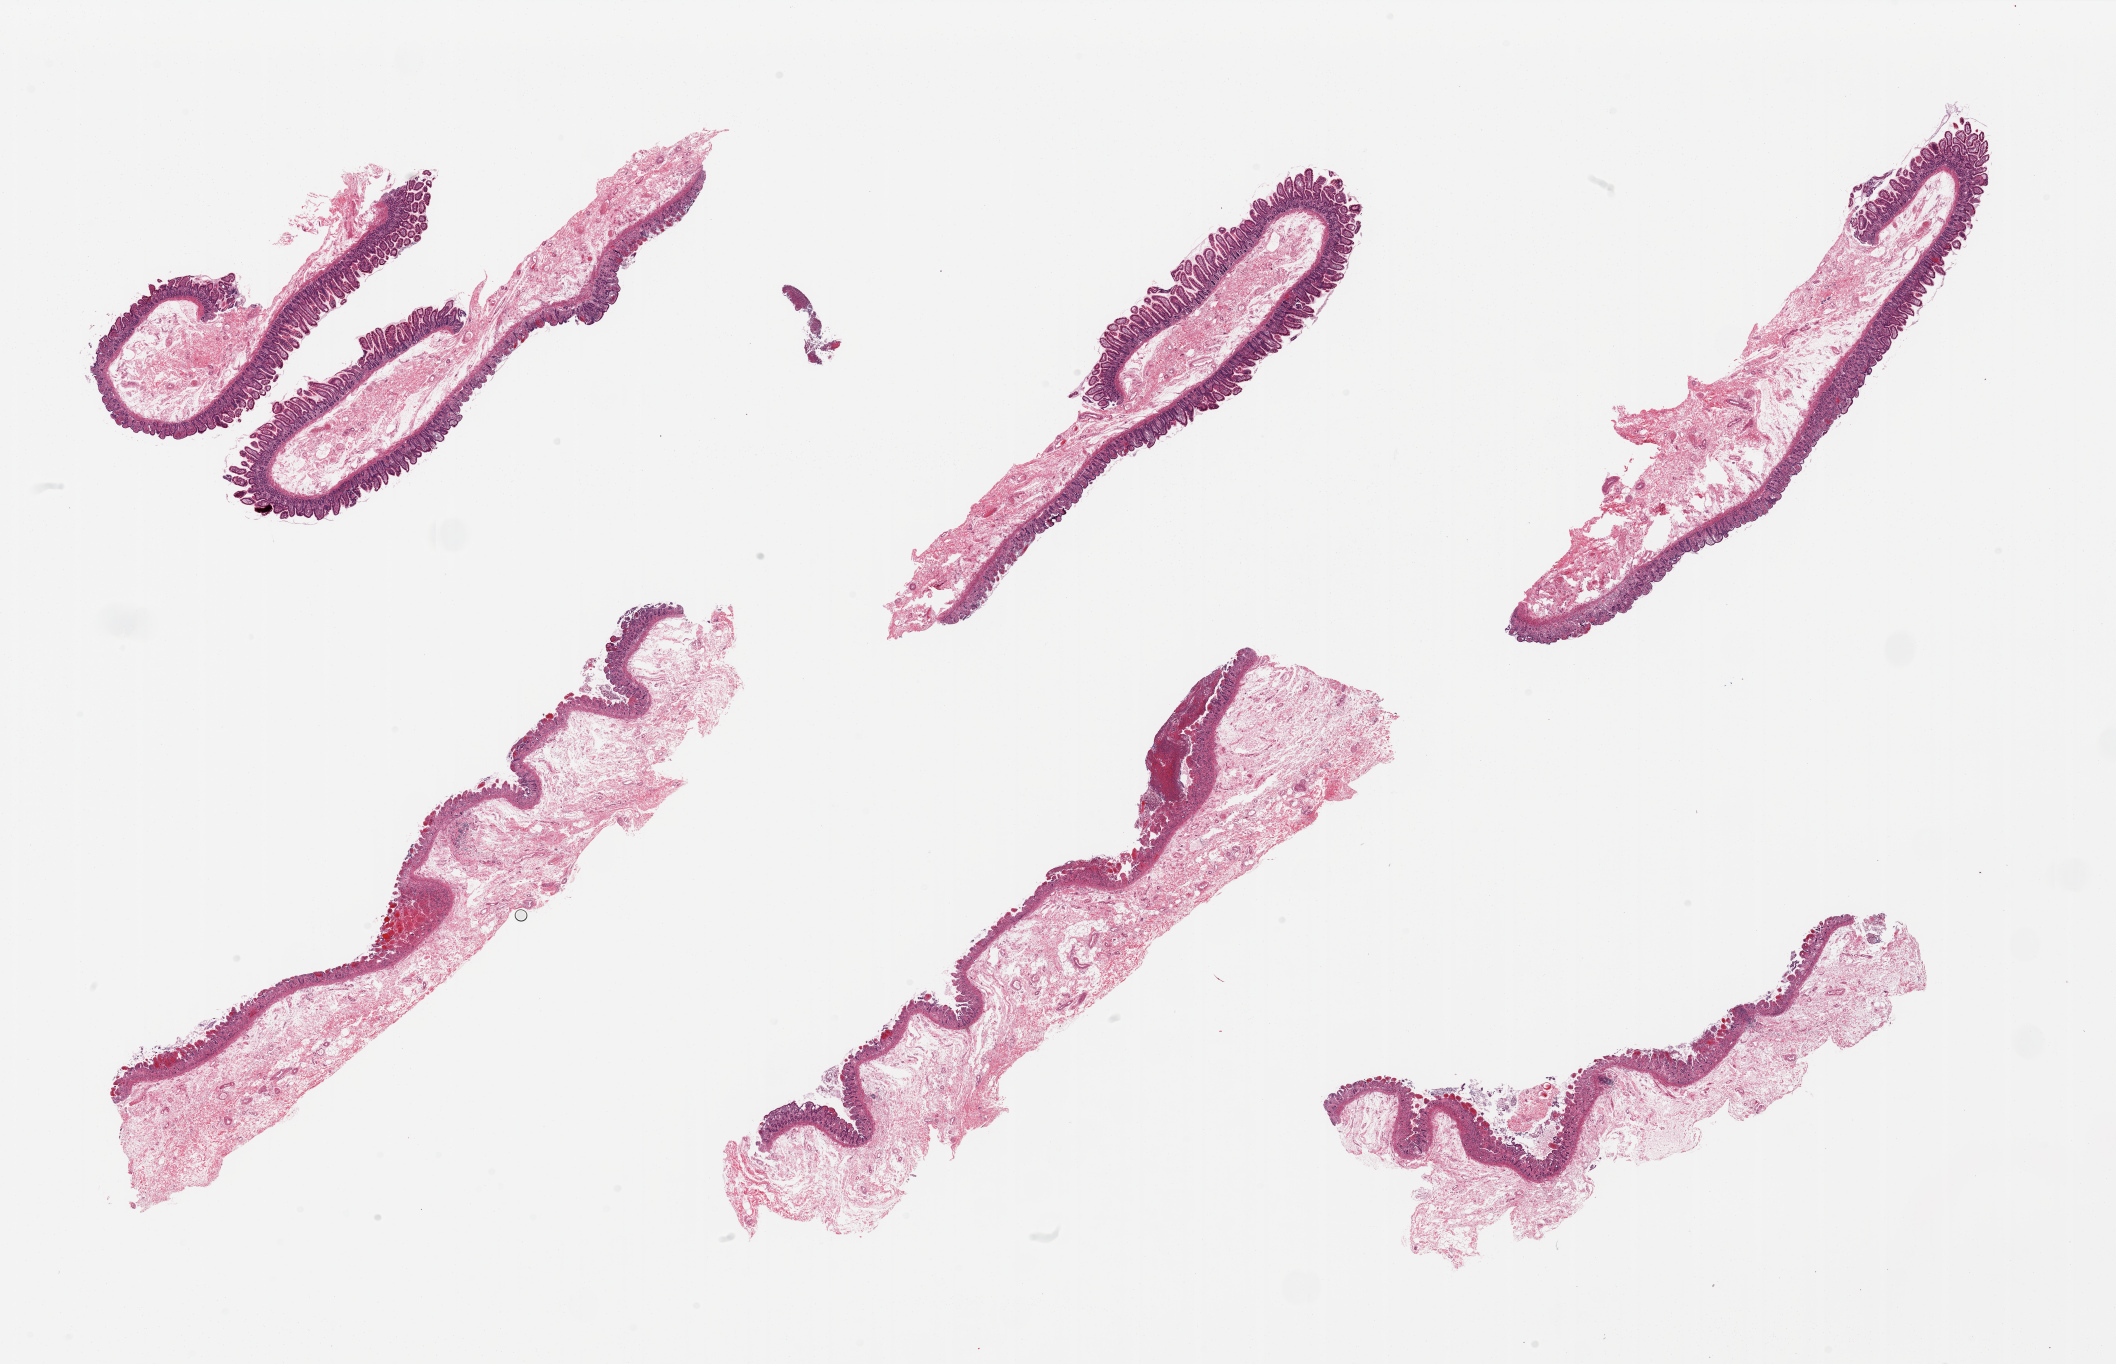
H&E whole-slide image, brightfield — shown as a low-resolution overview of the whole scanned area (about 33.5 x 21.6 mm, slide scanned at 20x), PAXgene-fixed paraffin-embedded (PFPE) section, sampled site (target tissue): ileum, tissue donor sample. Female donor.
- review note (as recorded): 6 pieces, mucosa variably preserved, rare lymphoid aggregates